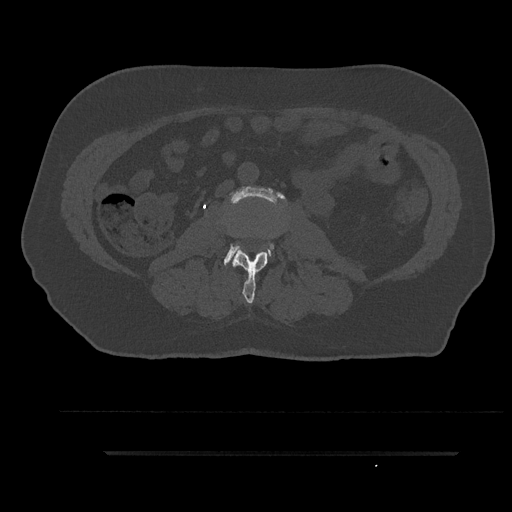
CT including the spine, one axial slice. Slice 77 of 797 in the series (ordered by position). Reconstruction kernel Br40s/3. 120 kVp. Bone window (W 1800 / L 400 HU). 512 × 512 image matrix, field of view 432 × 432 mm. Patient: male, 63 years. Case-level facts recorded for this patient, not image findings: primary cancer: renal; vertebrae with lytic lesions (as recorded): T8.
Outlined on this slice (semi-automatically segmented with operator editing):
- L2 vertebra: bounding box [x1, y1, x2, y2] px = [232, 251, 268, 304]
- L3 vertebra: [224, 187, 285, 265]